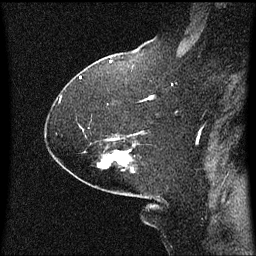
Breast MRI (dynamic contrast-enhanced), one sagittal slice. Slice 40 of 60 in the series (ordered by position). Dynamic contrast-enhanced series, image 2 of 3 at this slice position (ordered by acquisition). 1.5 T. TE 4.2 ms, TR 8 ms. 2.1 mm slice thickness. 256 × 256 image matrix, field of view 200 × 200 mm. Female patient, age 59 years.
Annotated regions visible in this slice (semi-automatically segmented with operator editing):
- analysis volume of interest (the breast-tissue region the enhancement analysis was run in; not a lesion): bounding box [x1, y1, x2, y2] px = [84, 150, 135, 173]
- tumour enhancement mask (voxels above the 70 % enhancement threshold inside the analysis volume of interest): [110, 150, 131, 161]